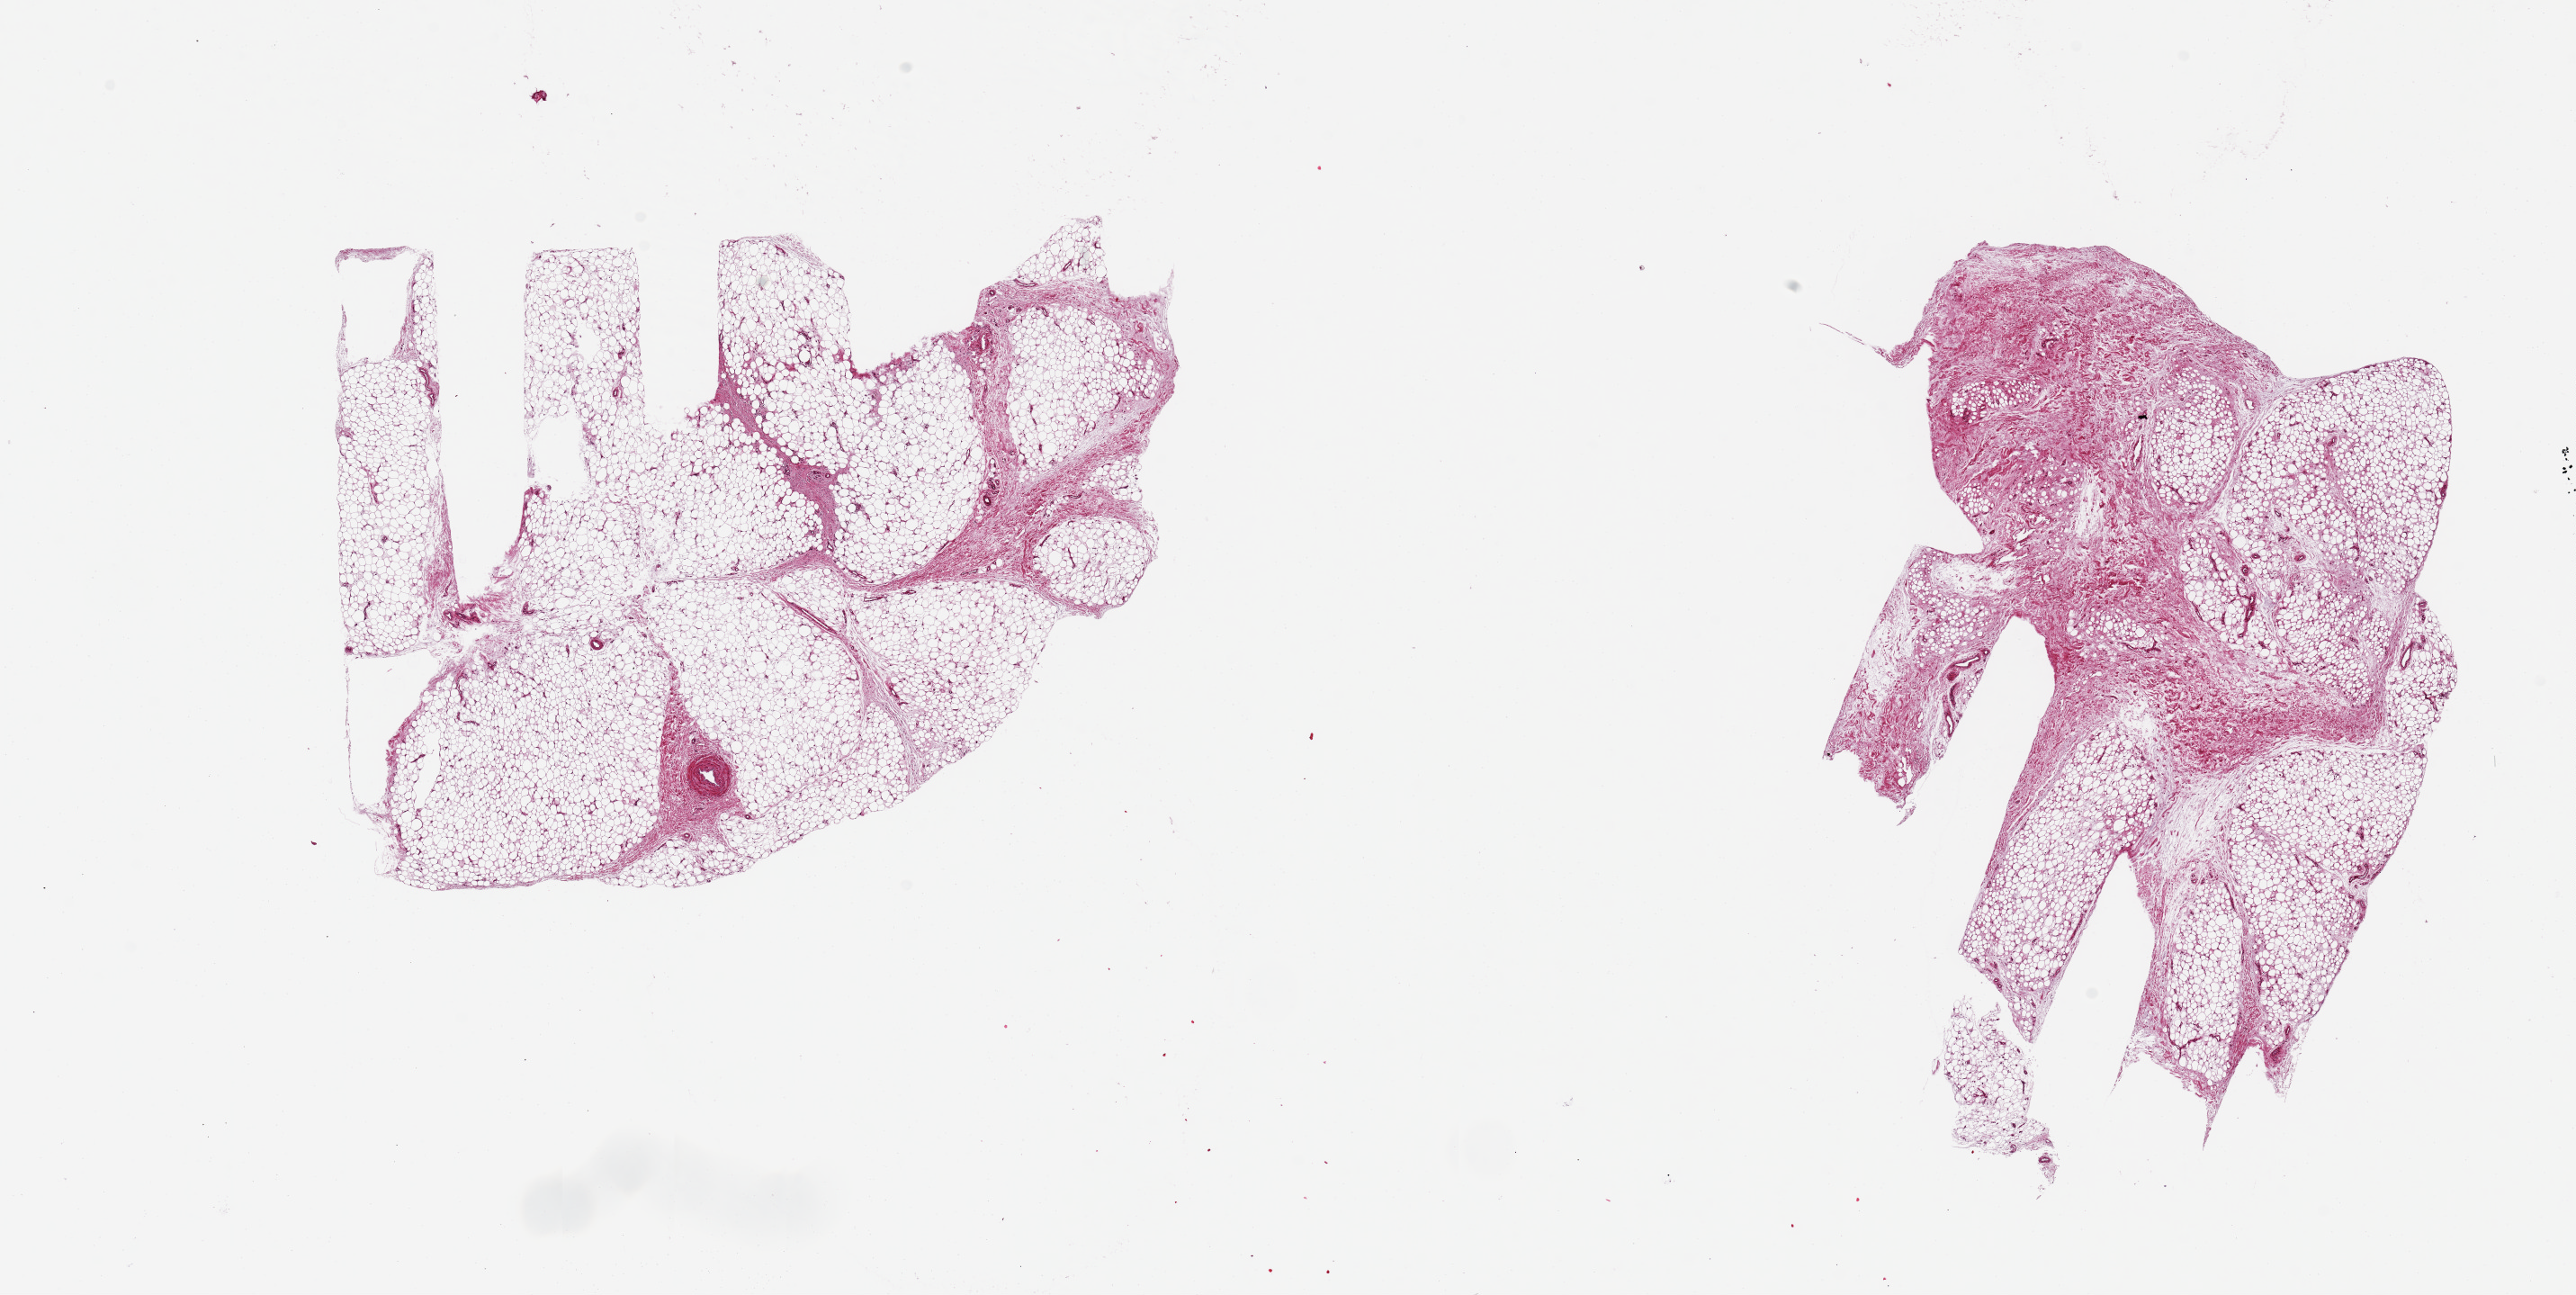
Haematoxylin and eosin whole-slide image, a low-resolution overview of the entire scanned area, about 22.6 x 11.4 mm (from a 20x scan), PAXgene-fixed, paraffin-embedded tissue, section of adipose tissue (target tissue), tissue donor sample. Donor sex: female.
Pathologist's review note for this sample: 2 pieces ~7x6mm.